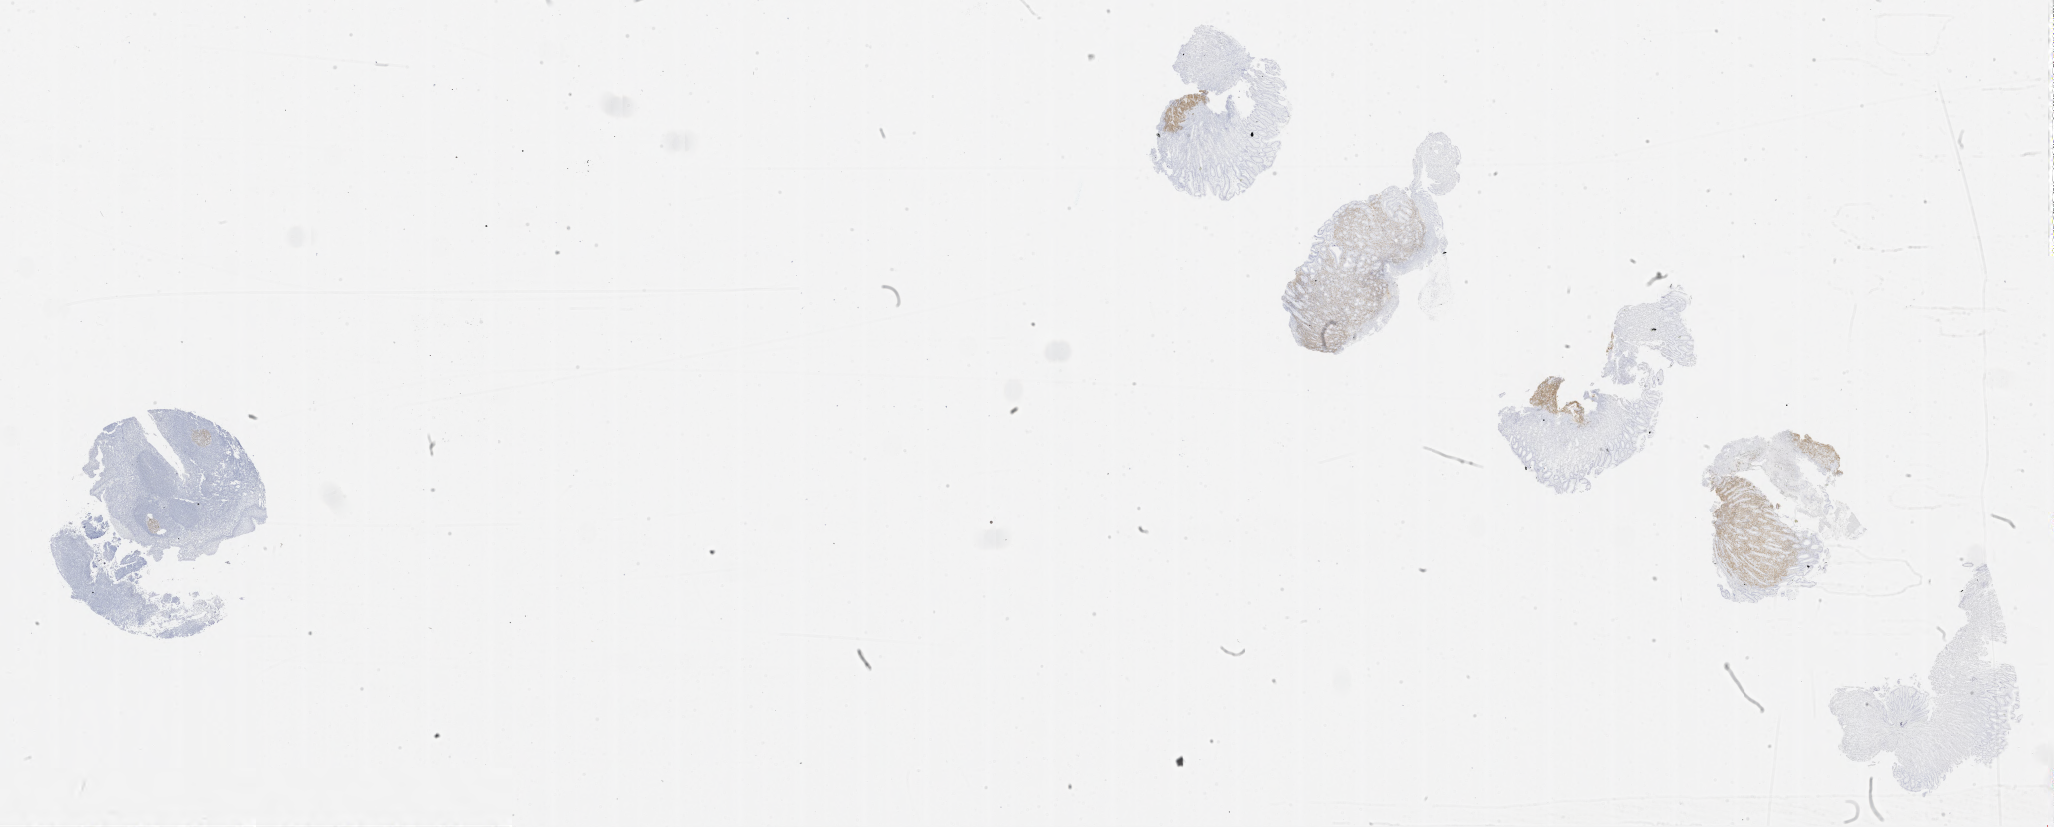
Whole-slide image, immunohistochemical stain for BCL6, low-resolution overview of the scanned area, about 33.0 x 13.3 mm. Tumor tissue. Patient male; aged 40.
Diagnosis: Burkitt lymphoma, NOS.